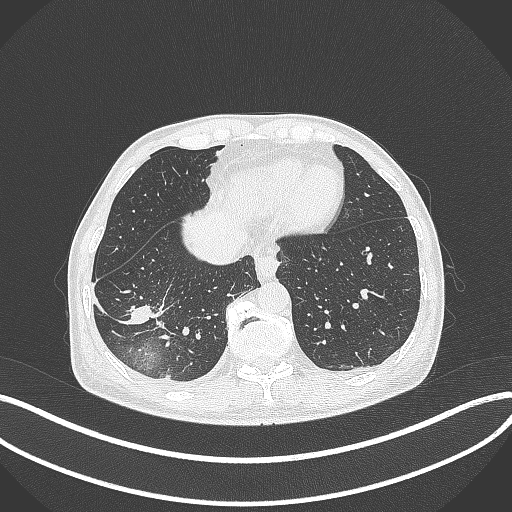
Chest CT, one axial slice; slice 95 of 388 in the series (ordered by position); reconstruction kernel B70f; 120 kVp; lung window (W 1500 / L -600 HU); 1 mm slice thickness; 512 × 512 image matrix. Male patient, age 64 years. Case-level facts recorded for this patient, not image findings: clinical TNM (as recorded): T3 N0 M0.
Structures marked on this image (bounding box drawn by a radiologist):
- lung tumour (recorded histology: adenocarcinoma): box from (x=122, y=295) to (x=170, y=330) px